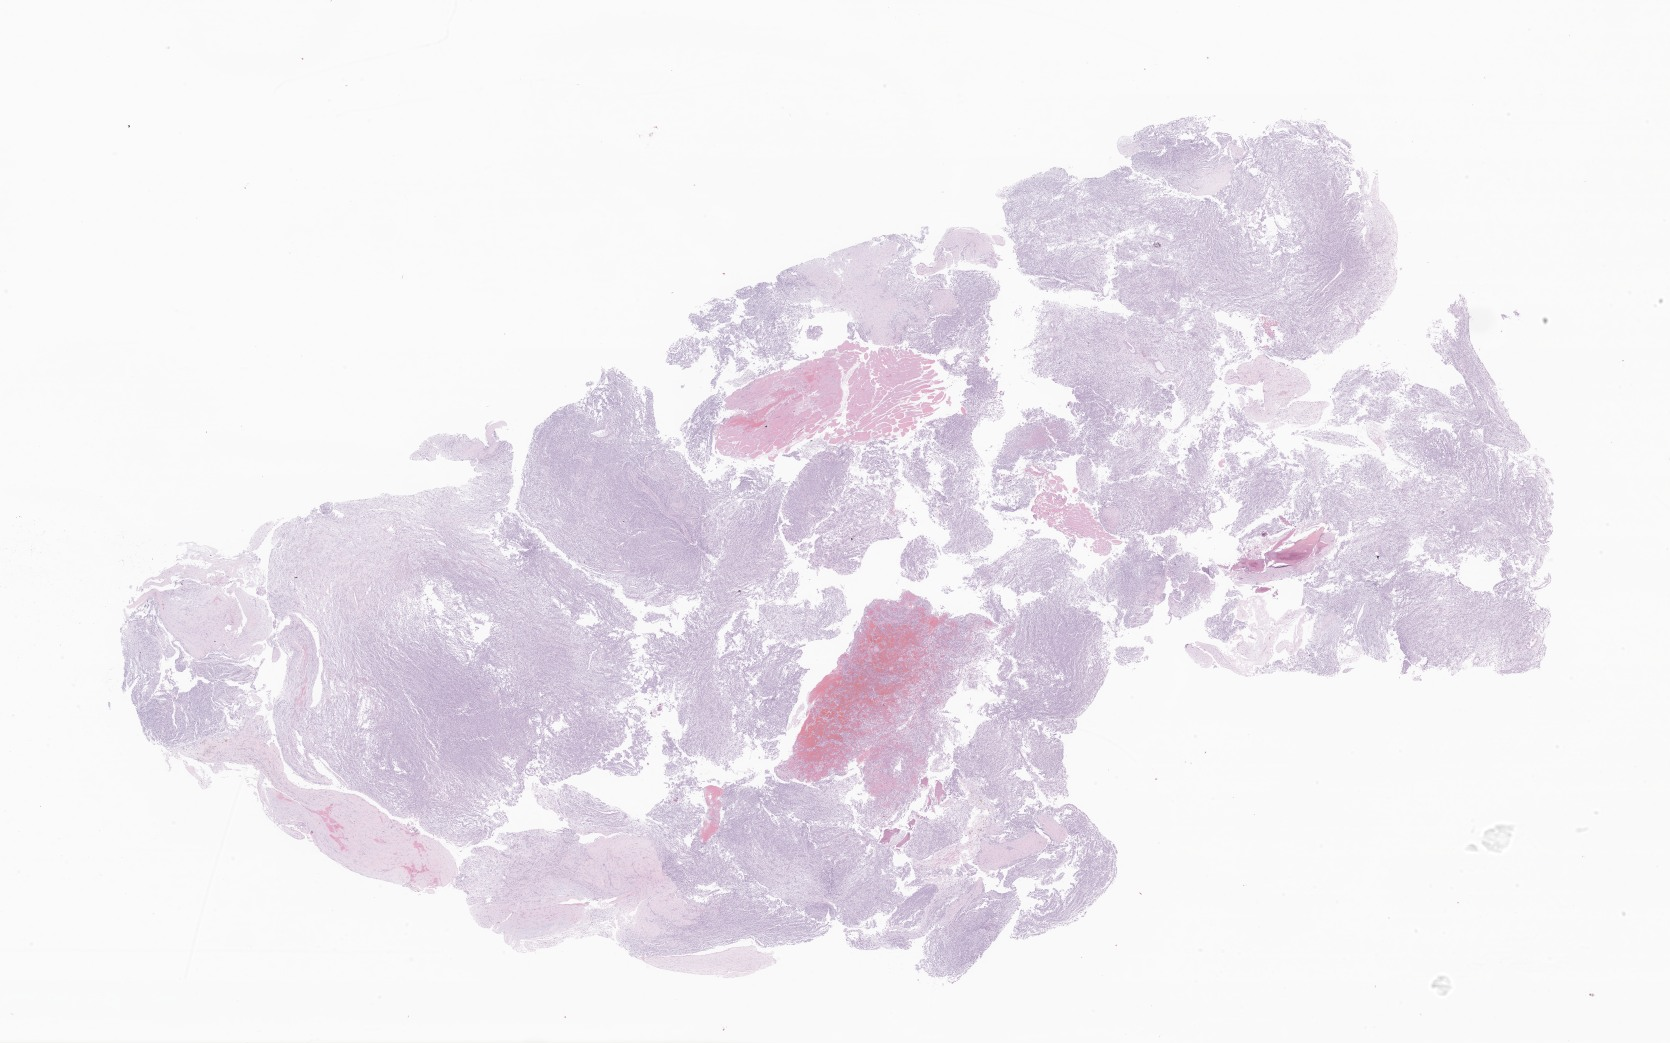
Digitized hematoxylin and eosin (H&E)-stained section of tumor tissue from the lower limb — shown as a low-resolution overview of the whole scanned area (about 28.2 x 17.6 mm). Formalin-fixed paraffin-embedded section. Patient: male, age 109 months.
• diagnosis (ICD-O-3 morphology term): Neoplasm, malignant